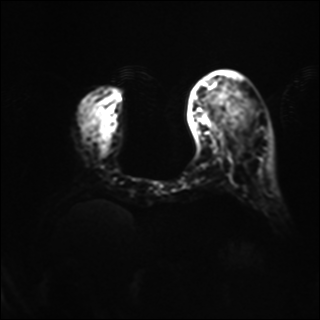
Breast MRI, one axial slice; position 14 of 40 along the scan axis; diffusion-weighted series; image 2 of 4 stored at this slice position (different b-values; order by instance number); 1.5 T; 320 × 320 image matrix, field of view 320 × 320 mm. Female patient.
Structures marked on this image (manually delineated by an expert):
- tumour on diffusion-weighted imaging: bounding box <229,98,249,113> (left, top, right, bottom; pixels)